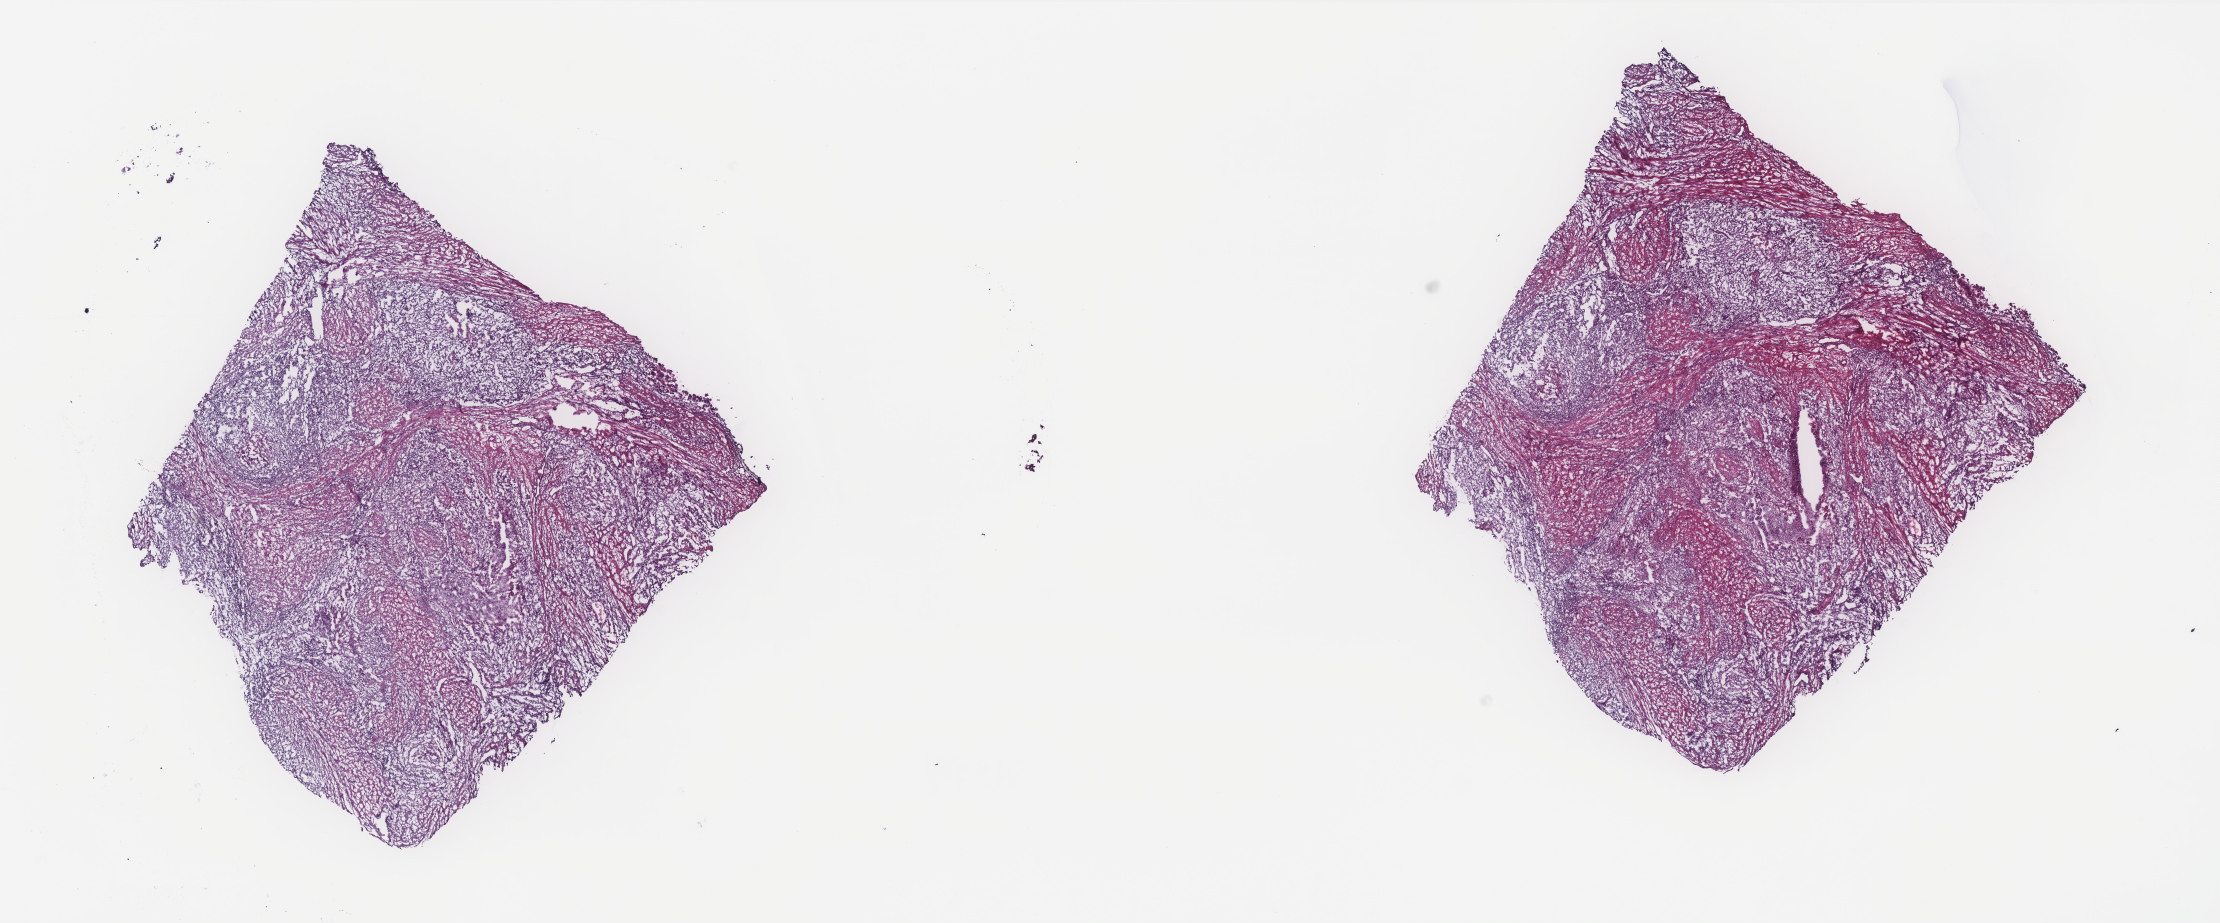
Digitized H&E tissue section (whole slide), whole scanned area (about 17.8 x 7.4 mm, from a 40x scan) shown as a low-resolution overview. Frozen section from the top of the tissue portion. Uterus, primary tumour sample. Female, age 45 years at initial diagnosis. Histologic grade: G3 (poorly differentiated). Composition of this section per pathologist review: tumour cells 65%, tumour nuclei 60%, normal cells 0%, stromal cells 30%, necrosis 5%. Infiltration values recorded for this section: lymphocyte infiltration 0%, monocyte infiltration 0%, neutrophil infiltration 0%.
• pathologic diagnosis: Endometrioid adenocarcinoma, NOS
• FIGO stage: IIIC1